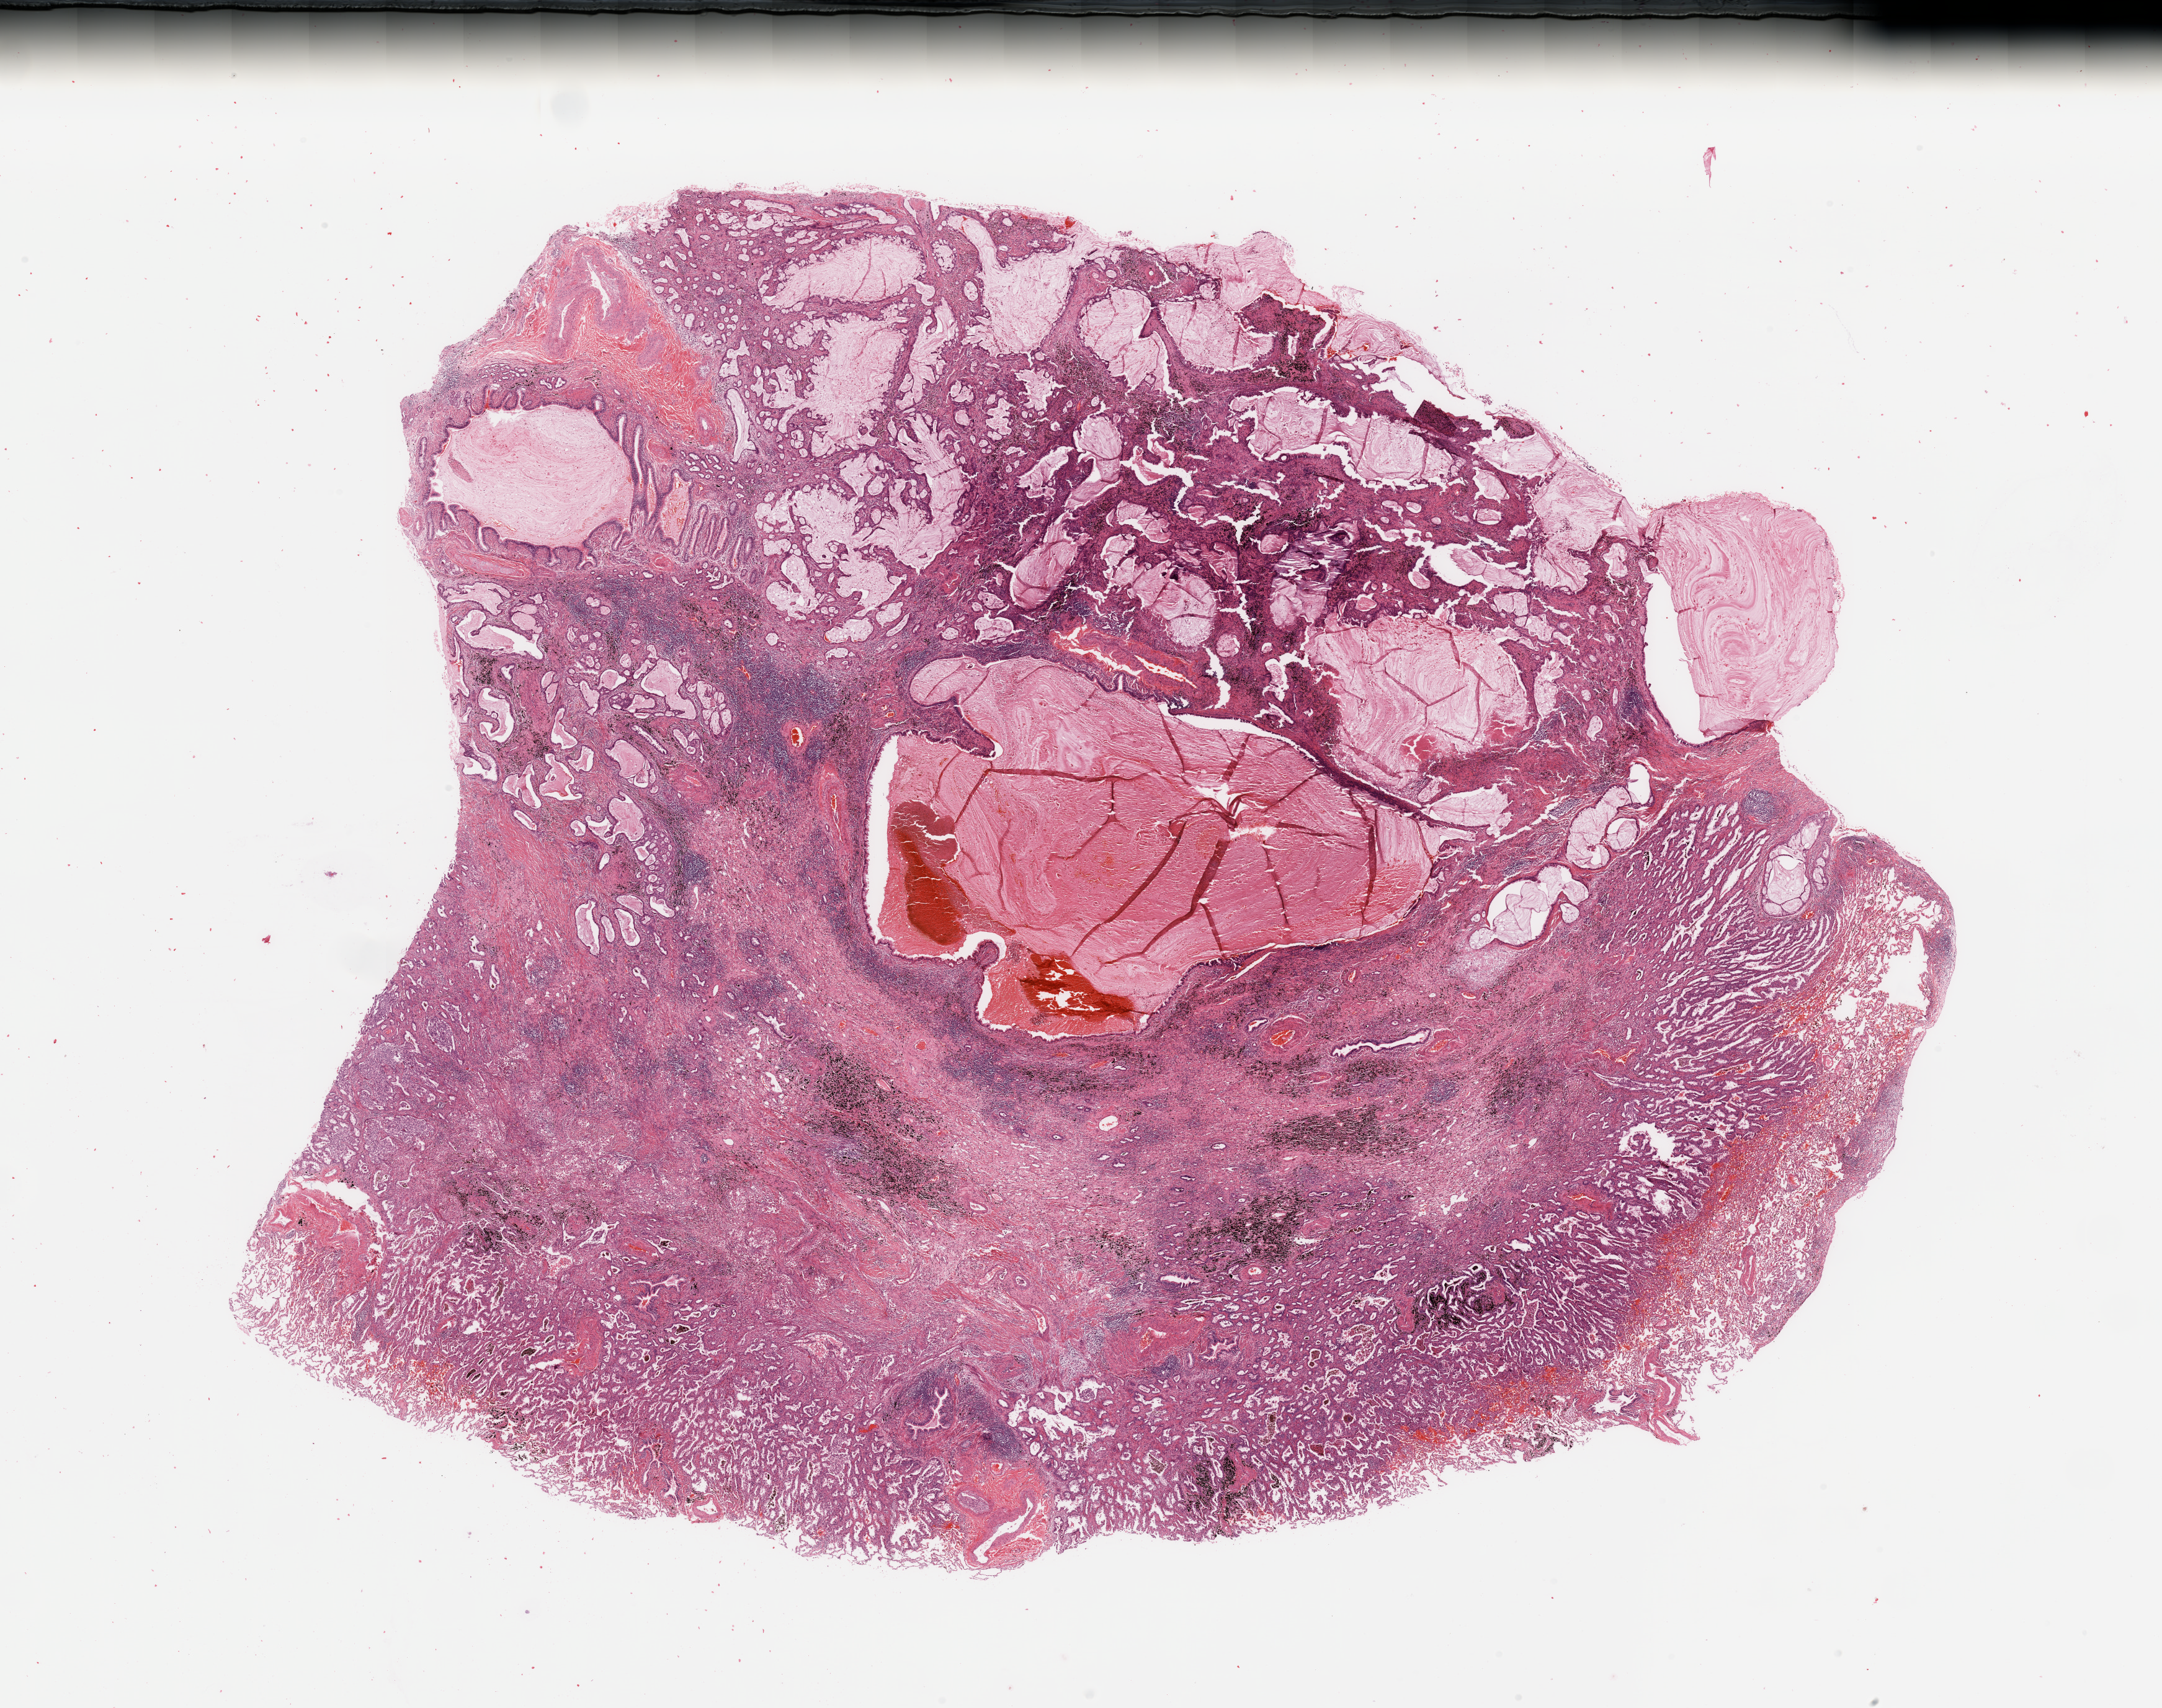
Hematoxylin and eosin (H&E) stained whole-slide image, a low-resolution overview of the entire scanned area, about 27.6 x 21.8 mm (from a 20x scan). Lung, tumour tissue. Patient: male, age 60 years. Histologic grade: G2 (moderately differentiated).
* diagnosis: Adenocarcinoma, NOS
* AJCC pathologic stage: IIB